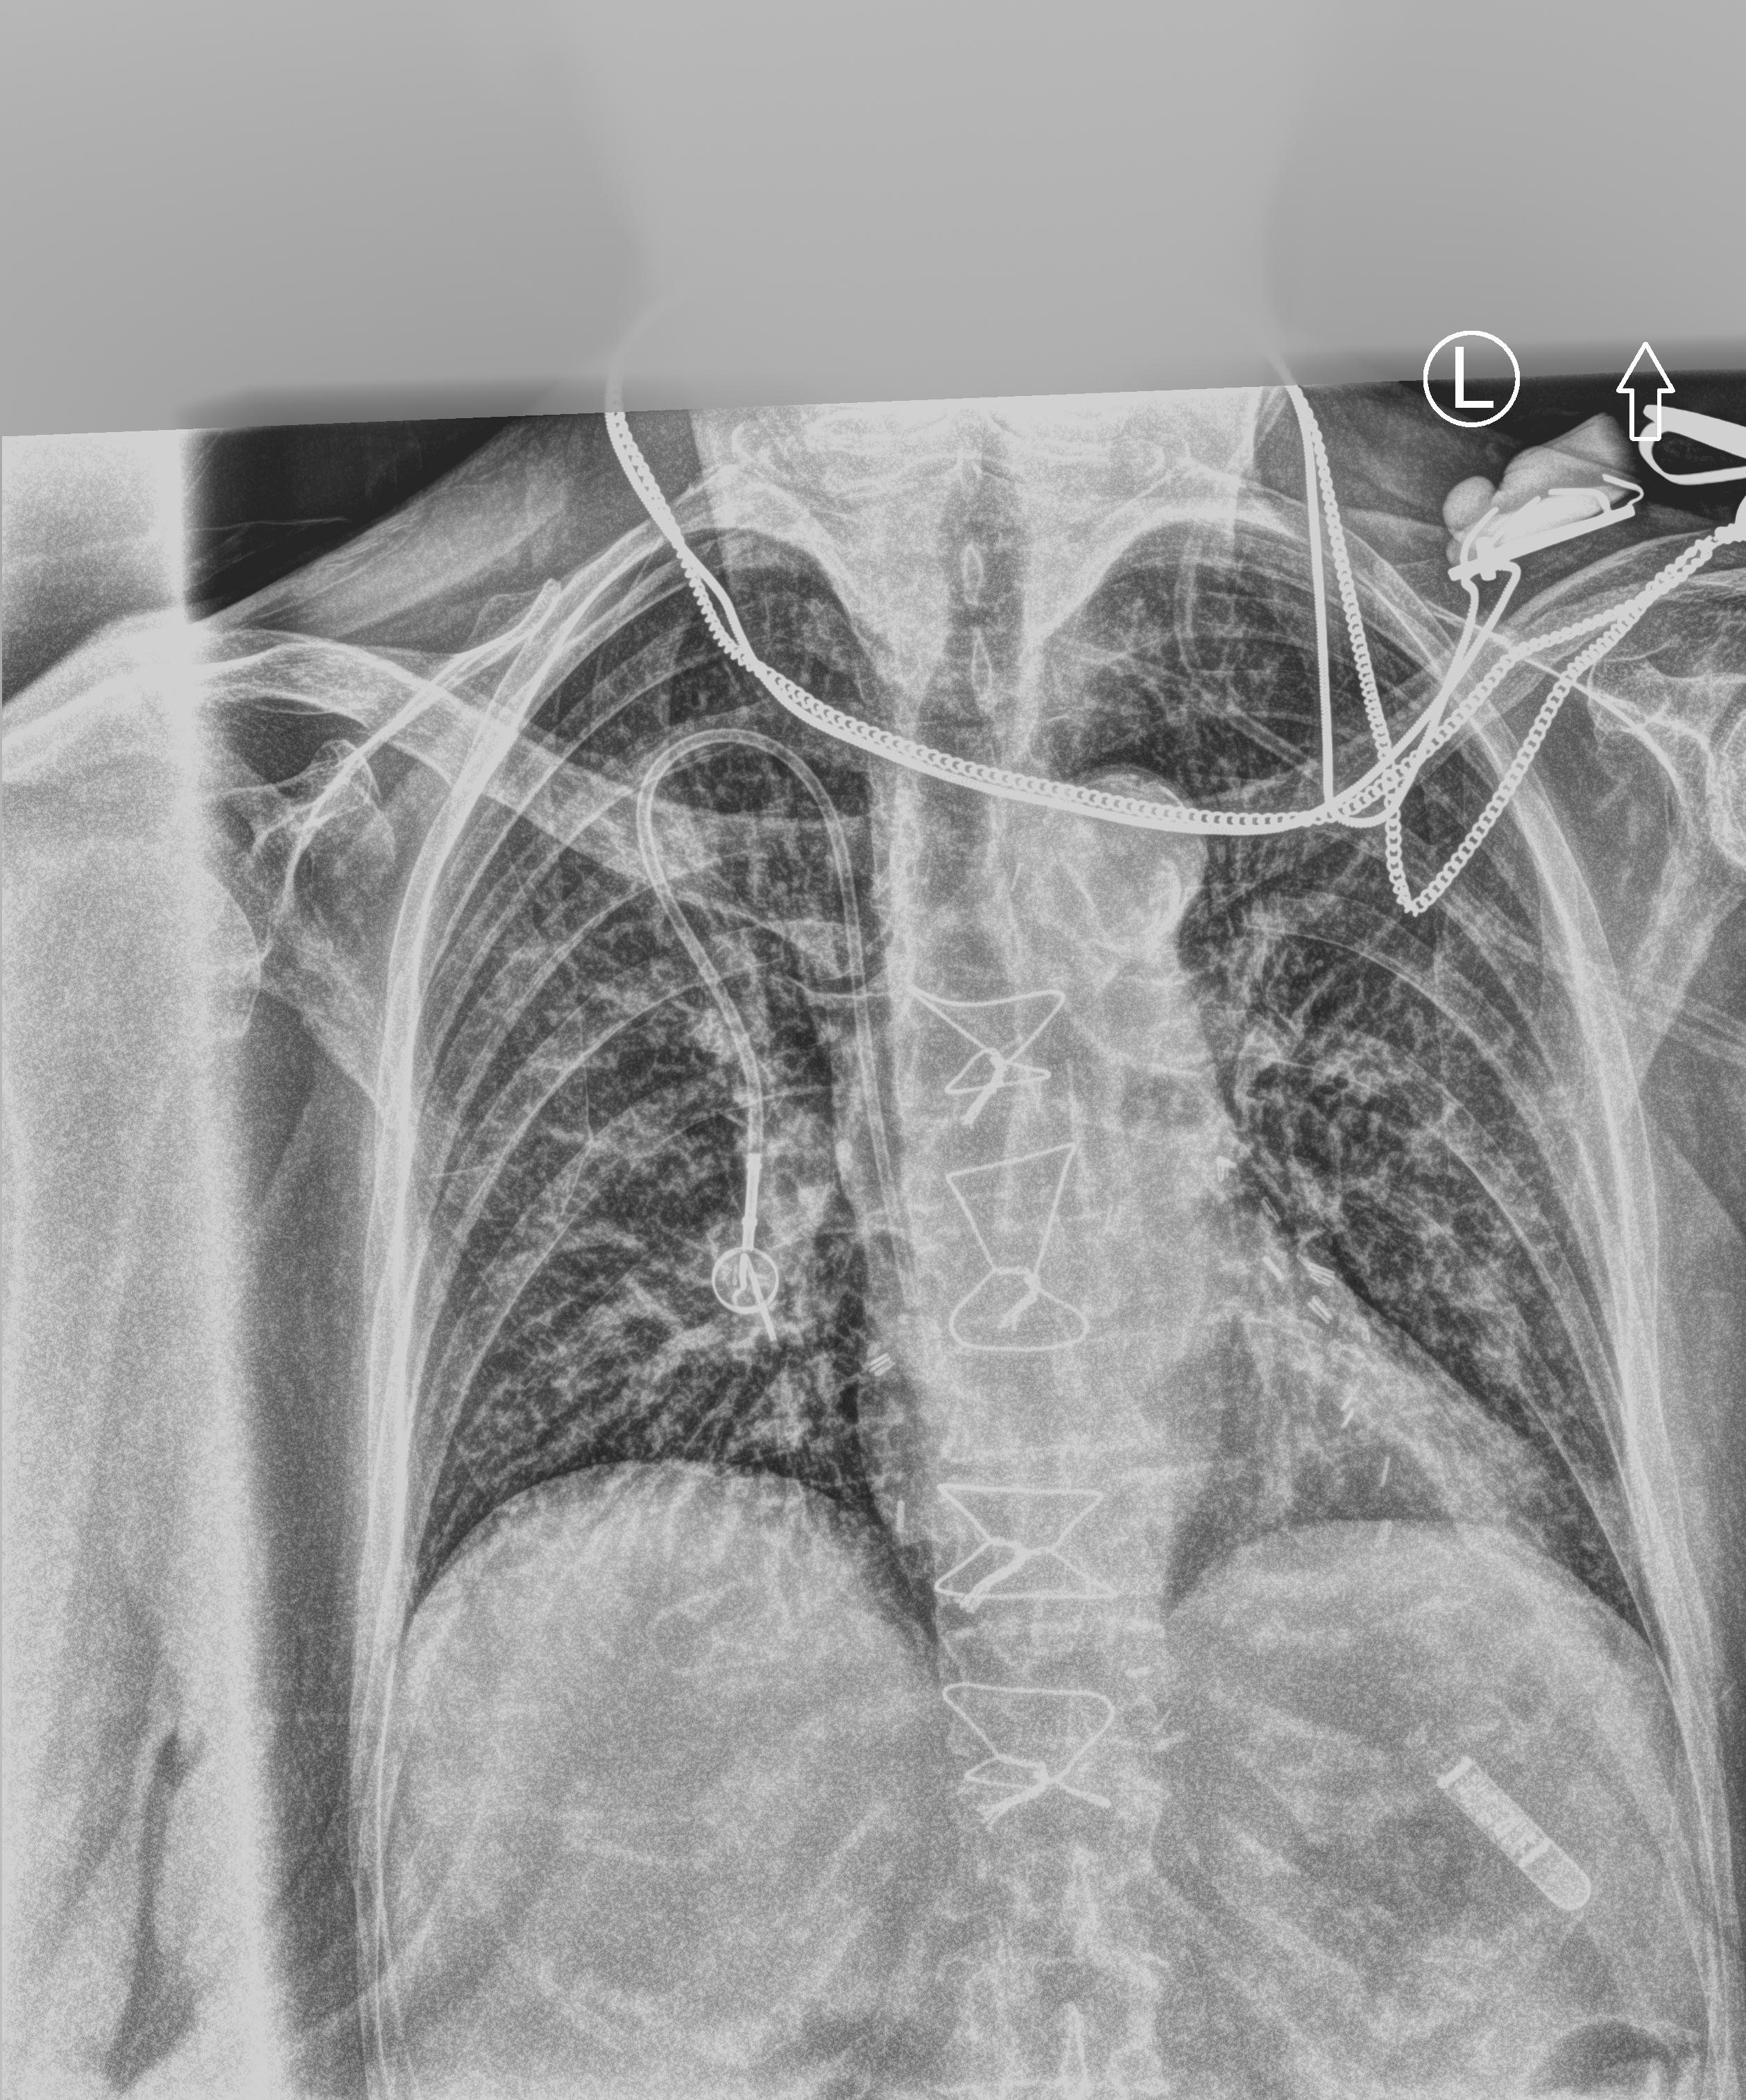
Chest X-ray (portable). Patient hospitalised with COVID-19; female, aged 75–90 years.
Hospital-stay facts (about this admission, not read from this image; timing relative to this image not recorded): chronic kidney disease (admission record): no; admitted to intensive care during this hospital stay: no.